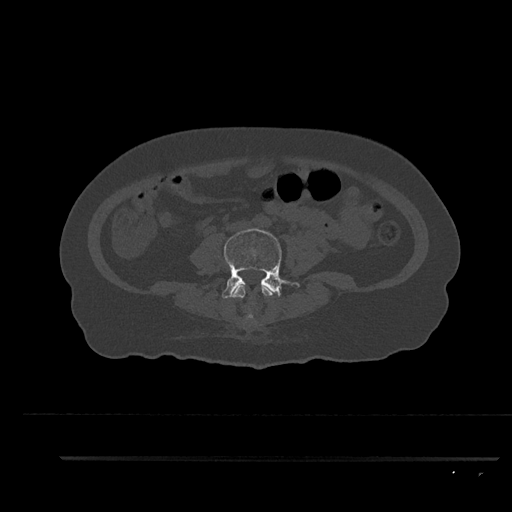
CT including the spine, one axial slice; position 40 of 797 along the scan axis; reconstruction kernel Br40s/3; 120 kVp; bone window (W 1800 / L 400 HU); 0.5 mm slice thickness; 512 × 512 image matrix. Female patient, age 44 years. From the clinical record (not read from this slice): primary cancer: renal; vertebrae with lytic lesions (as recorded): L1.
Outlined on this slice (semi-automatic segmentation, software-assisted and operator-edited):
- L3 vertebra: box from (x=232, y=284) to (x=280, y=320) px
- L4 vertebra: (x=221, y=228)–(x=300, y=299)